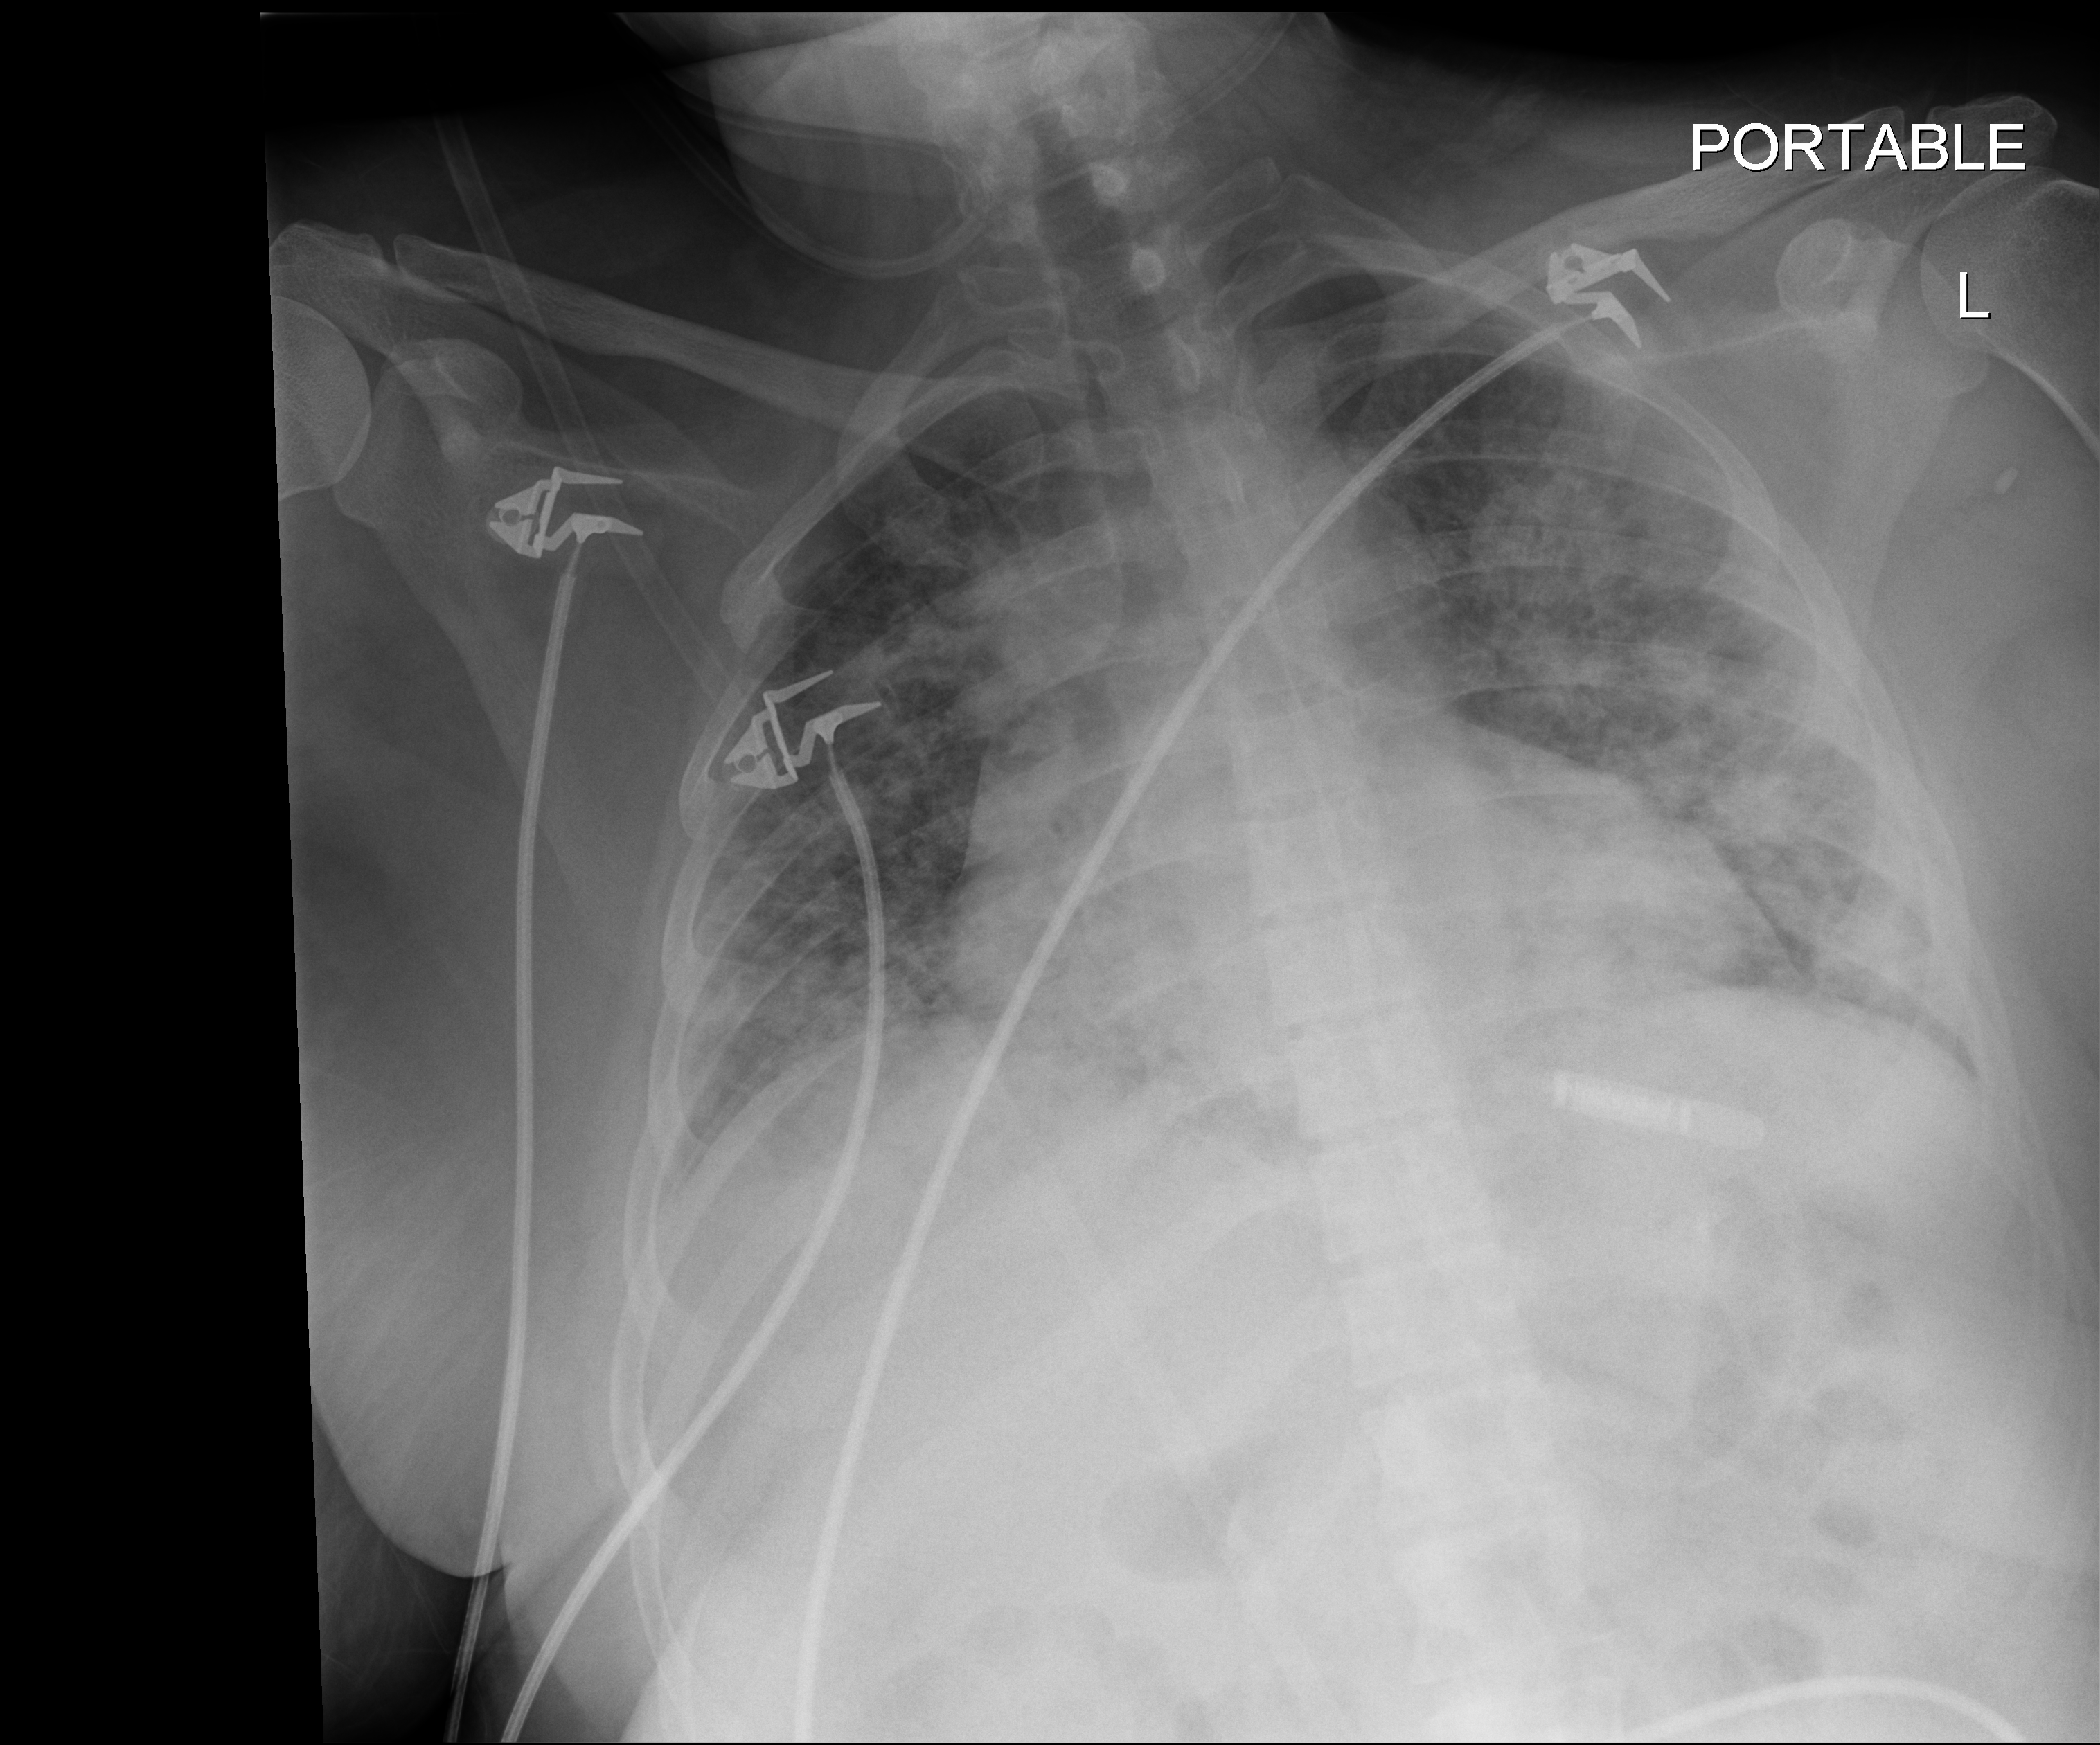
Bedside chest radiograph (digital radiography); anteroposterior (AP) projection. Female patient hospitalised with COVID-19, age 18–59 years.
Hospital-stay facts (about this admission, not read from this image; timing relative to this image not recorded):
- admitted to intensive care during this hospital stay: no
- mechanically ventilated during this hospital stay: yes